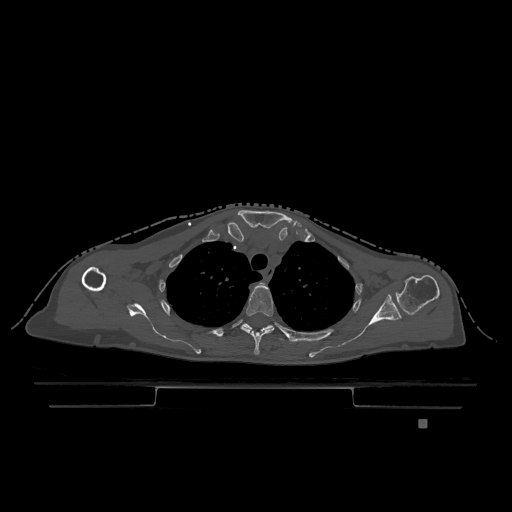
CT including the spine, one axial slice. Position 913 of 1317 along the scan axis. Bone window (W 1800 / L 400 HU). 0.5 mm slice thickness. 512 × 512 image matrix, field of view 500 × 500 mm. Patient: female, 74 years. From the clinical record (not read from this slice): primary cancer: lung.
Structures marked on this image (semi-automatically segmented with operator editing):
- T3 vertebra: bounding box <240,285,274,355> (left, top, right, bottom; pixels)
- T4 vertebra: <243,323,307,342>